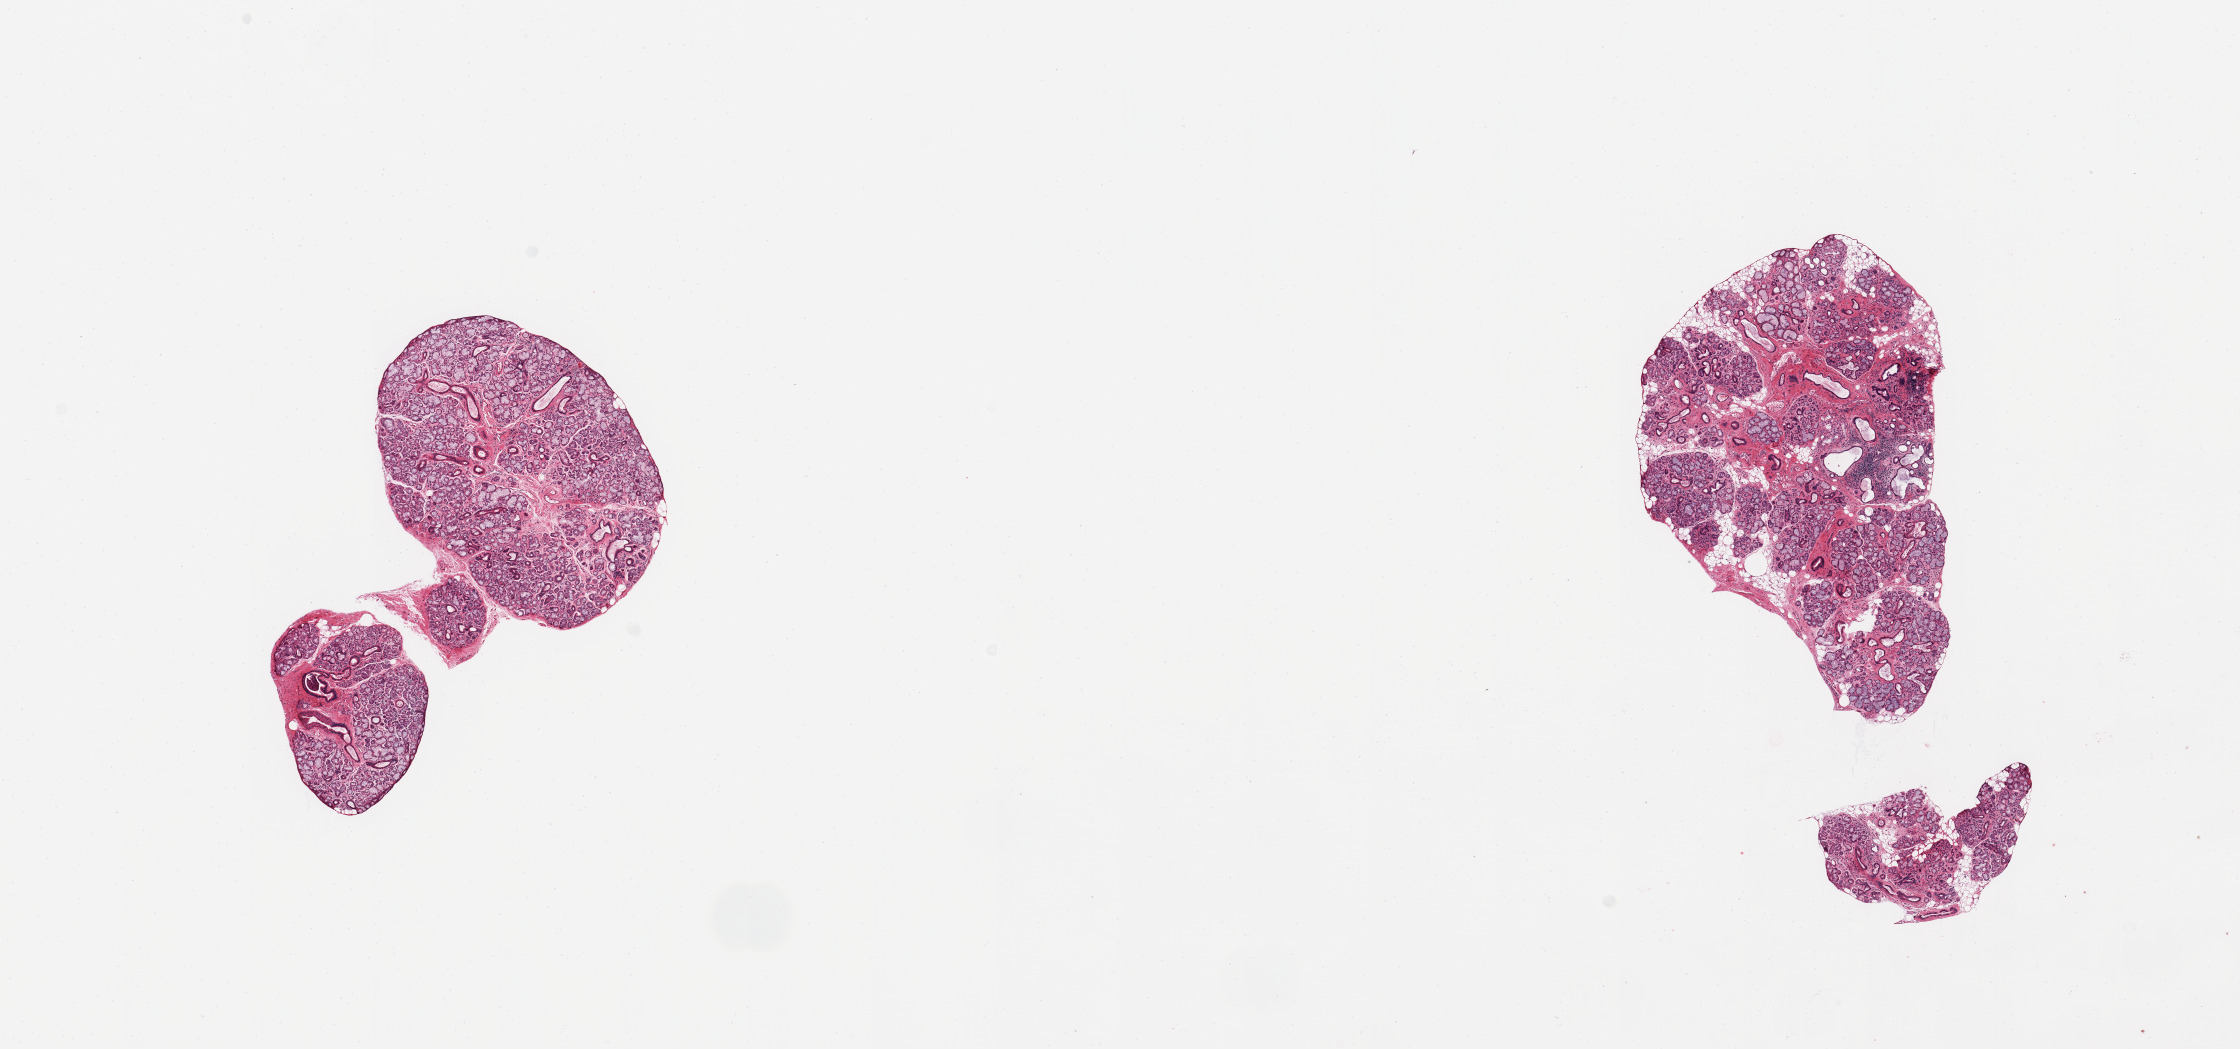
Digitized H&E-stained section, brightfield, whole scanned area (about 17.7 x 8.3 mm, from a 20x scan) shown as a low-resolution overview. PAXgene-fixed paraffin-embedded (PFPE) section. Section of minor salivary gland (target tissue). Donor tissue sample. Donor: male.
Reviewer comment on this tissue sample: 2 pieces; well trimmed, 1 piece includes small amount of internal fat and some chronic inflammation.